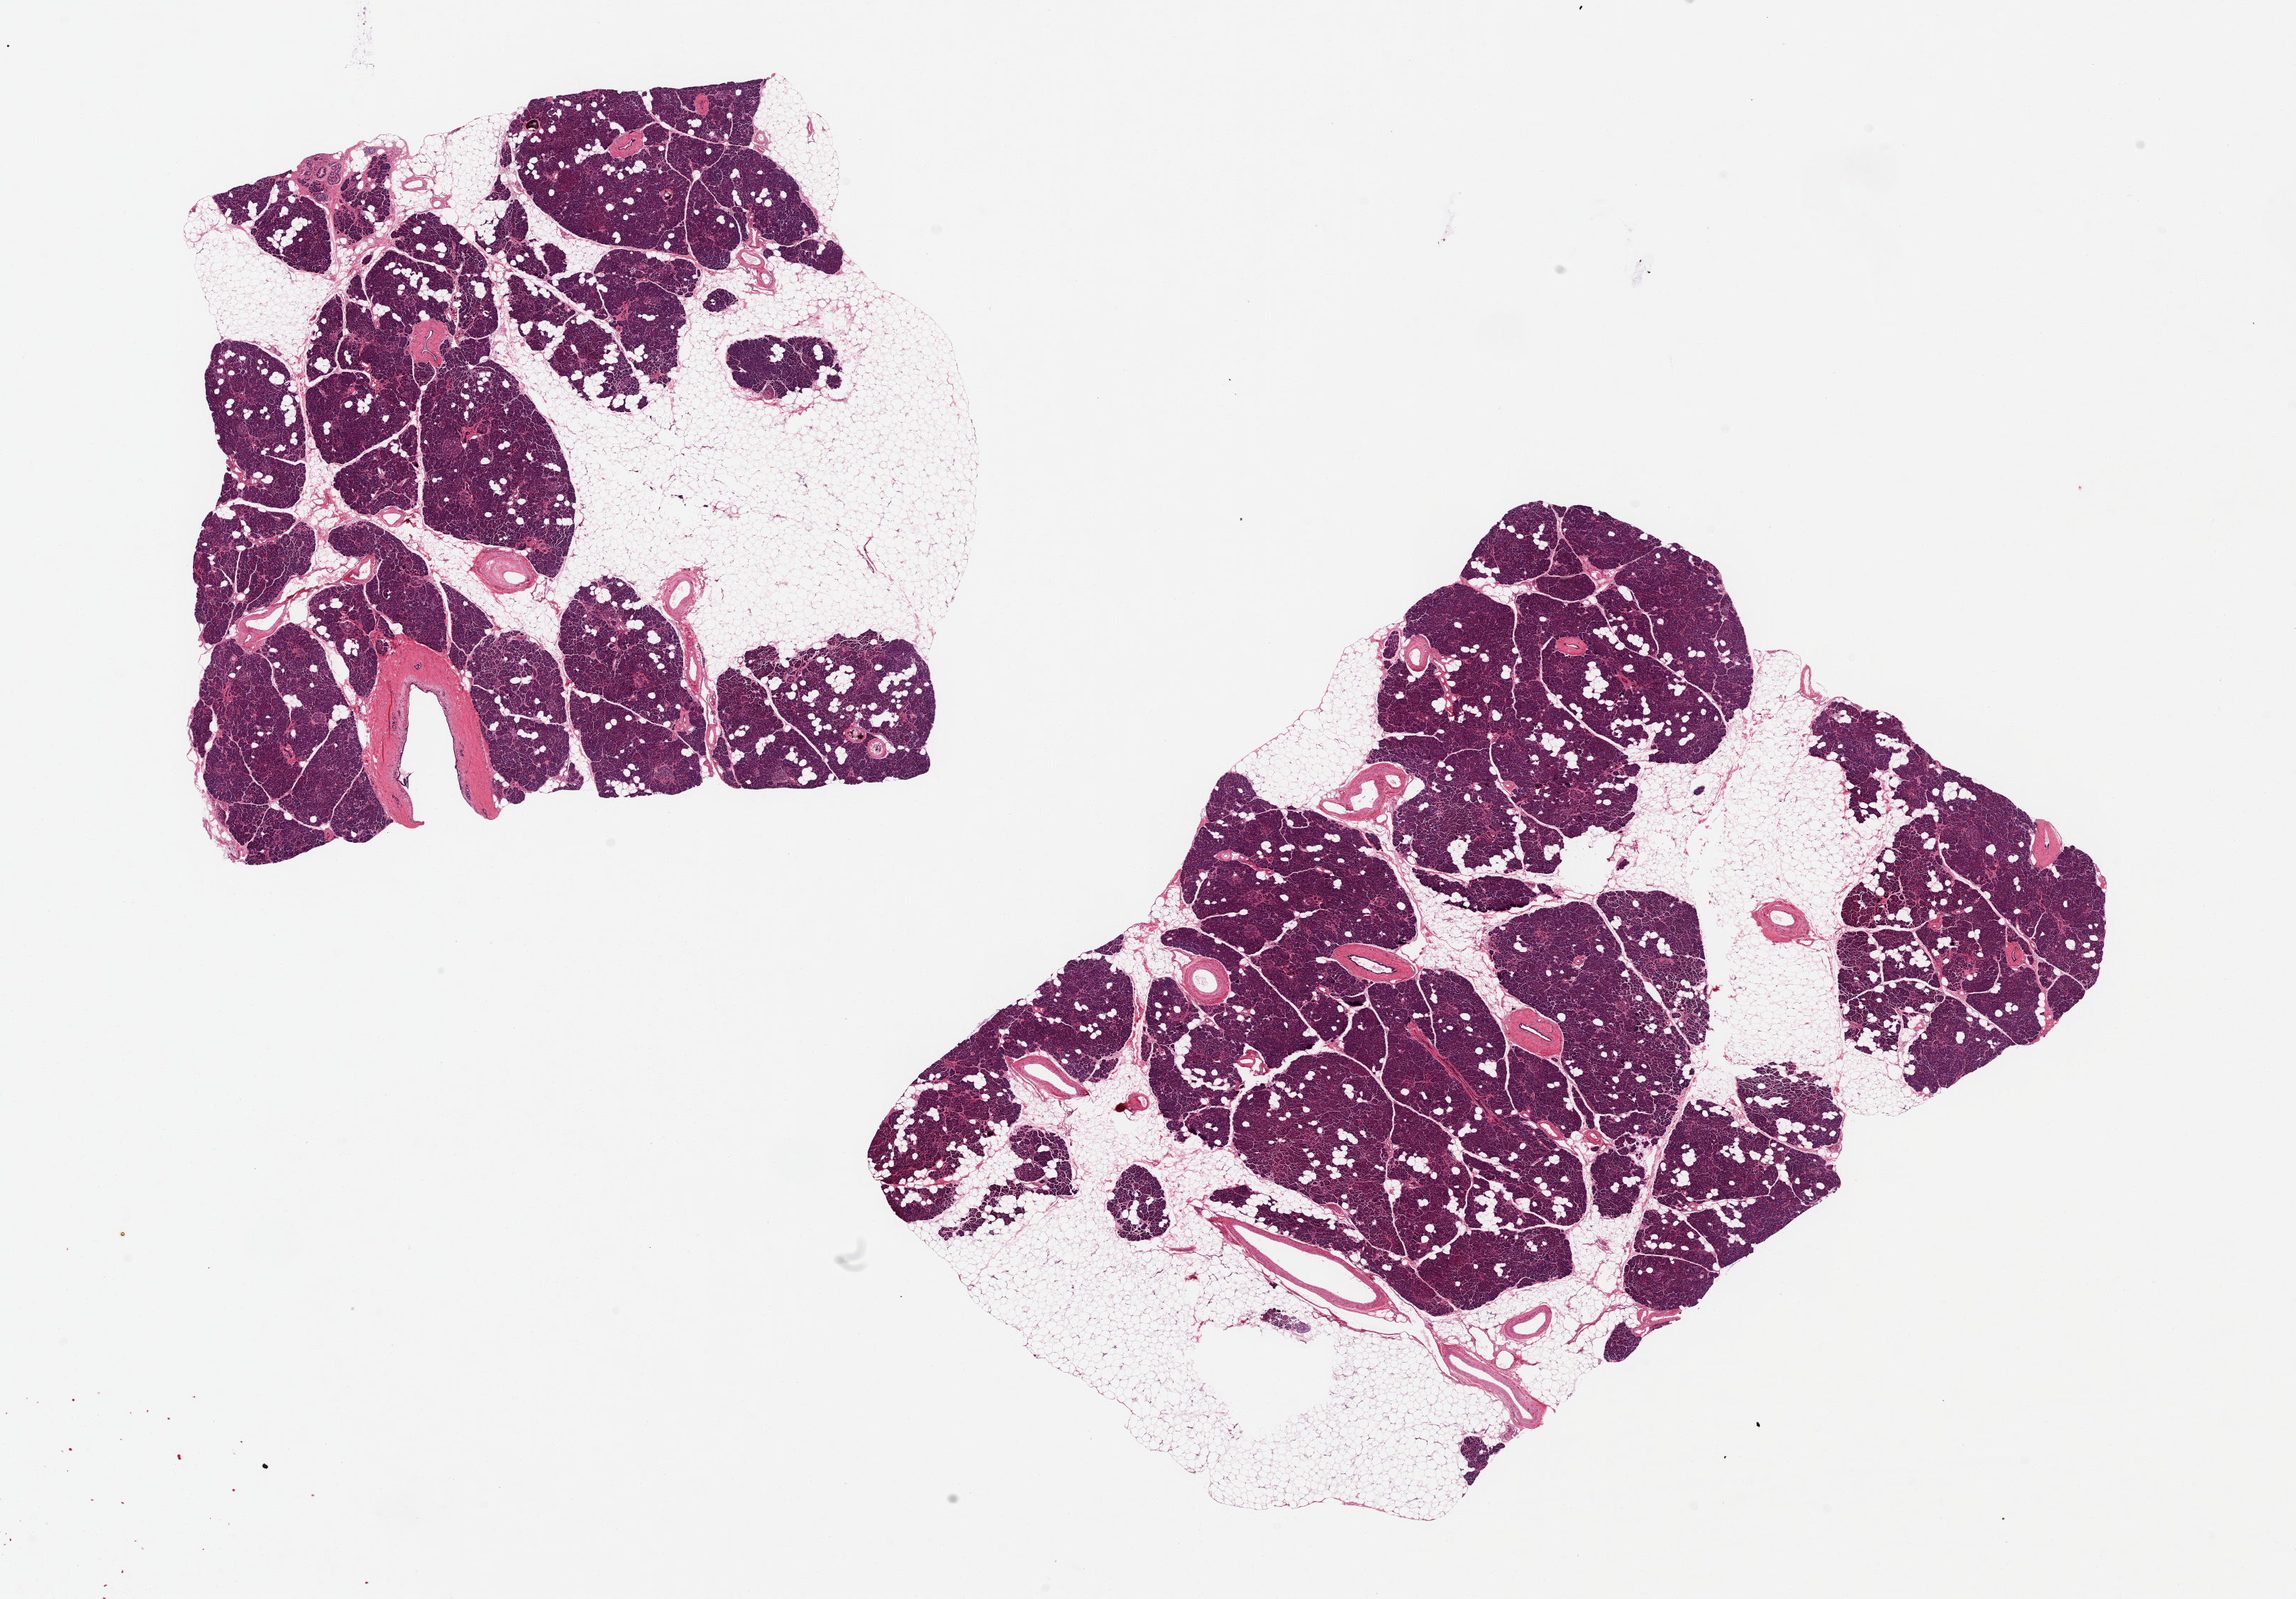
Hematoxylin and eosin (H&E) whole-slide image, brightfield, a low-resolution overview of the entire scanned area, about 25.6 x 17.8 mm; PAXgene-fixed paraffin-embedded (PFPE) section; target tissue: pancreas; tissue donor sample. Donor sex: male.
Pathologist's review note for this sample: 2 pieces 11x8 & 8x8 mm; ~50 % adipose intermingled with parenchyma; islets present.